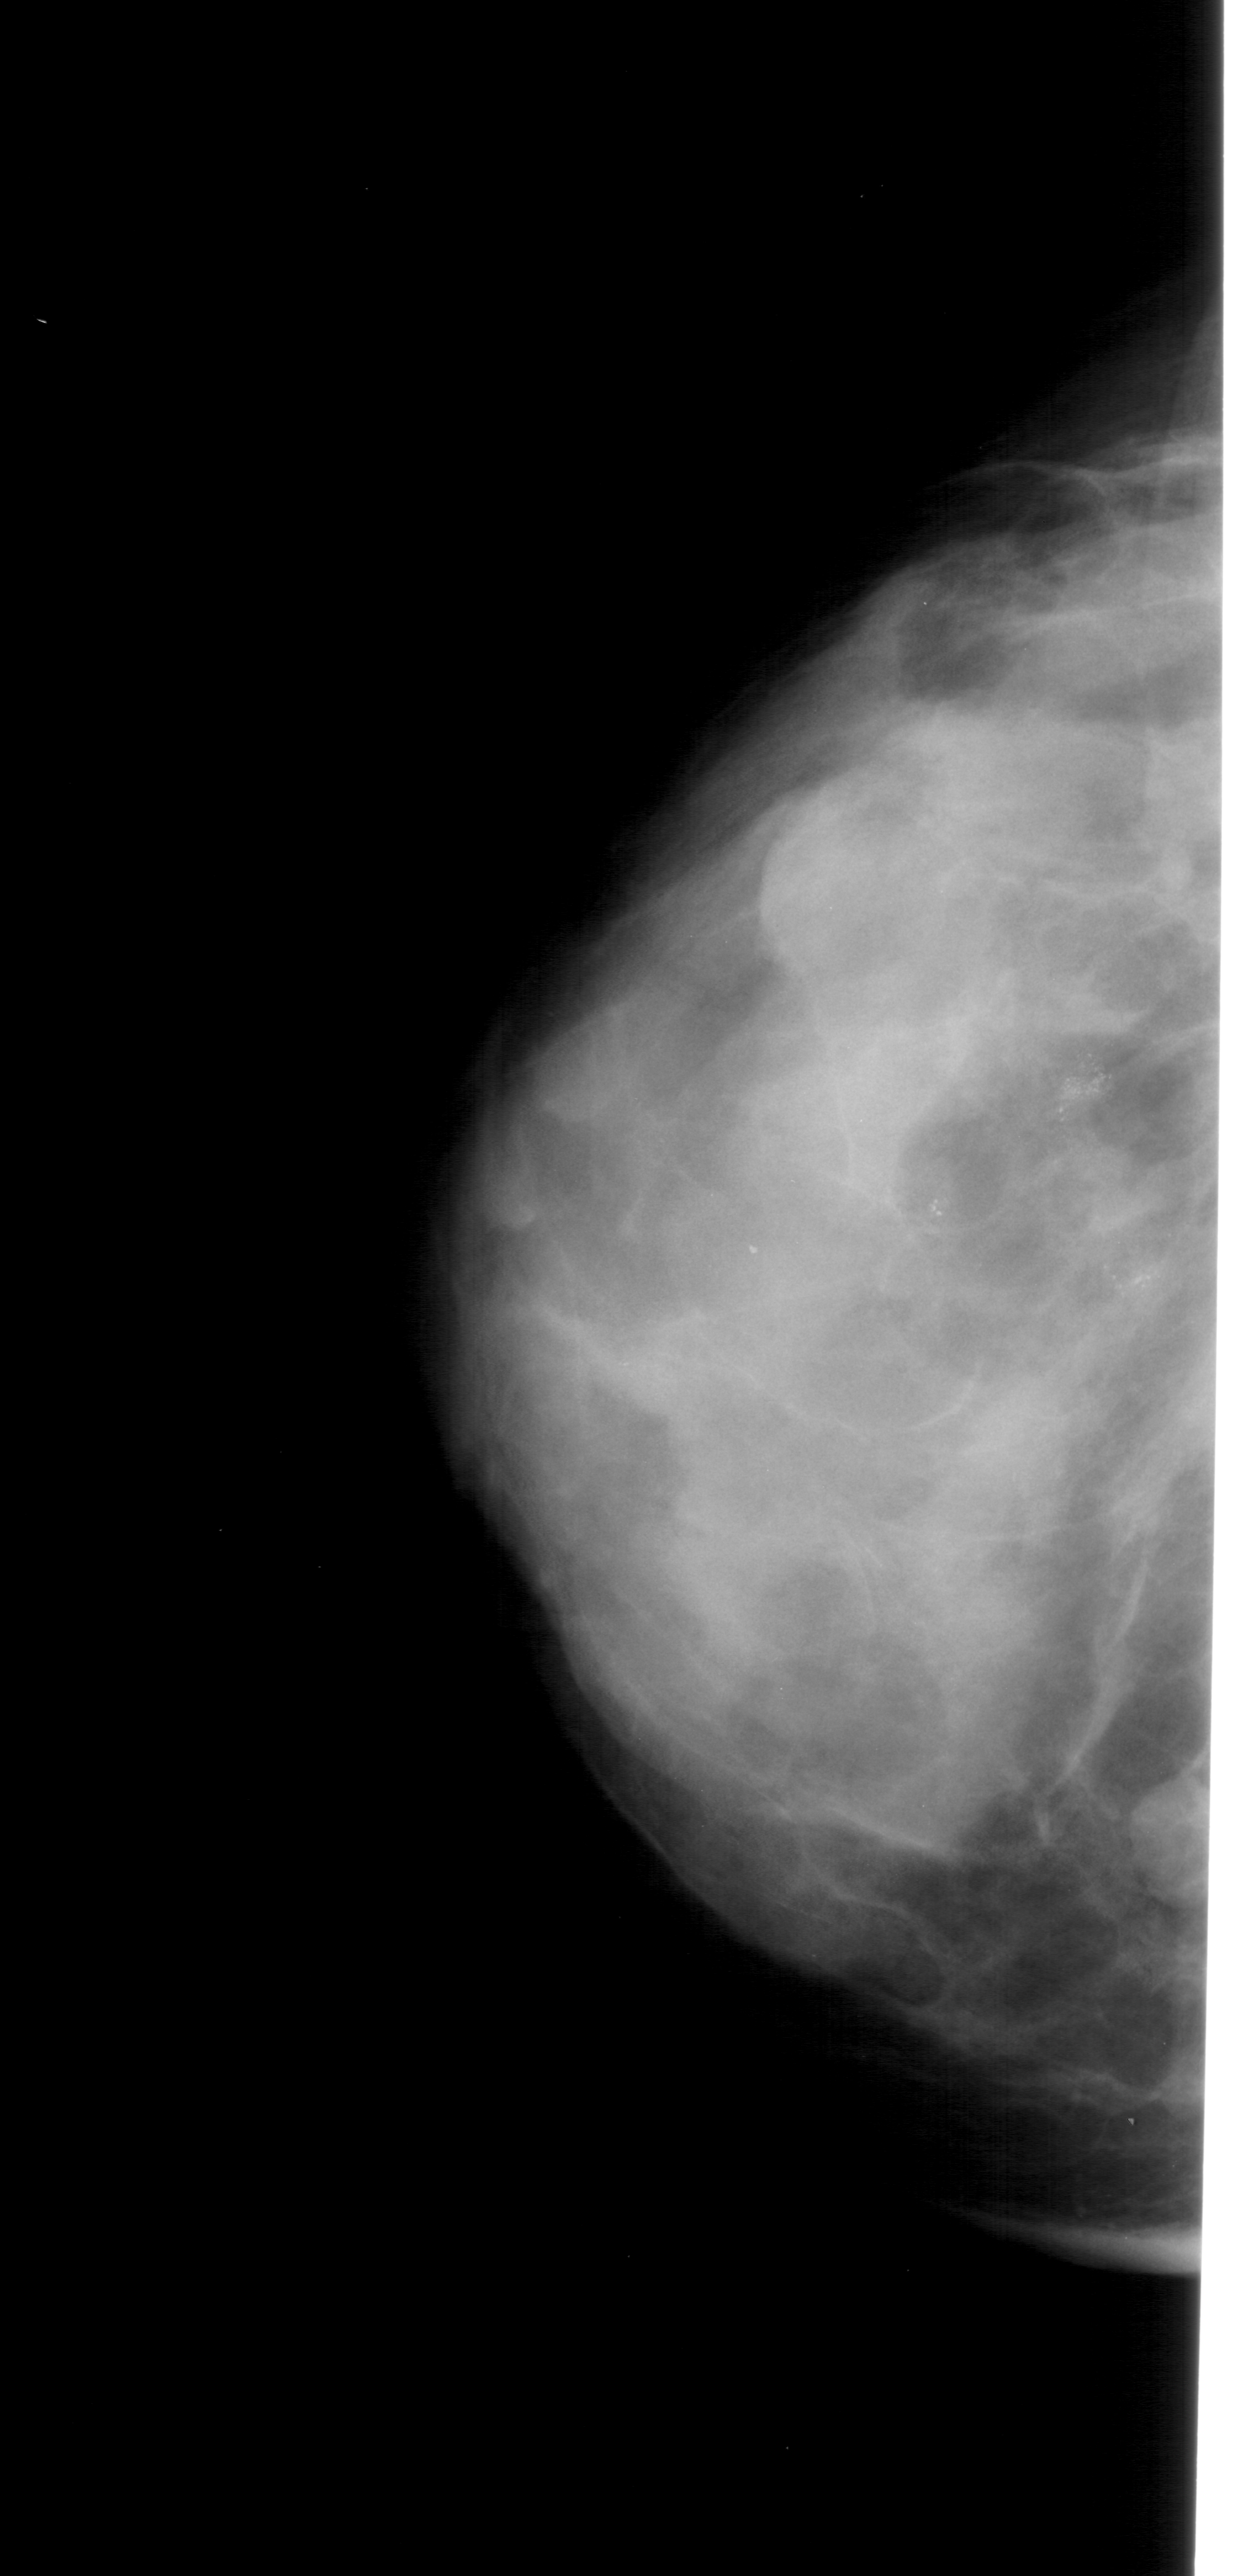
Mammogram (digitized film), left breast, craniocaudal (CC) view, breast composition: extremely dense (BI-RADS density category 4 of 4).
- Marked findings (only marked abnormalities are described; nothing is implied about the rest of the image): Finding 1 of 2: calcifications, morphology pleomorphic, distribution clustered; BI-RADS assessment category 4; subtlety rating 3 on a 1 (subtle) to 5 (obvious) scale; pathology result (as recorded, not read from the image): malignant.
- Finding 2 of 2: calcifications, morphology pleomorphic, distribution clustered; BI-RADS assessment category 4; subtlety rating 3 on a 1 (subtle) to 5 (obvious) scale; pathology (as recorded): malignant.